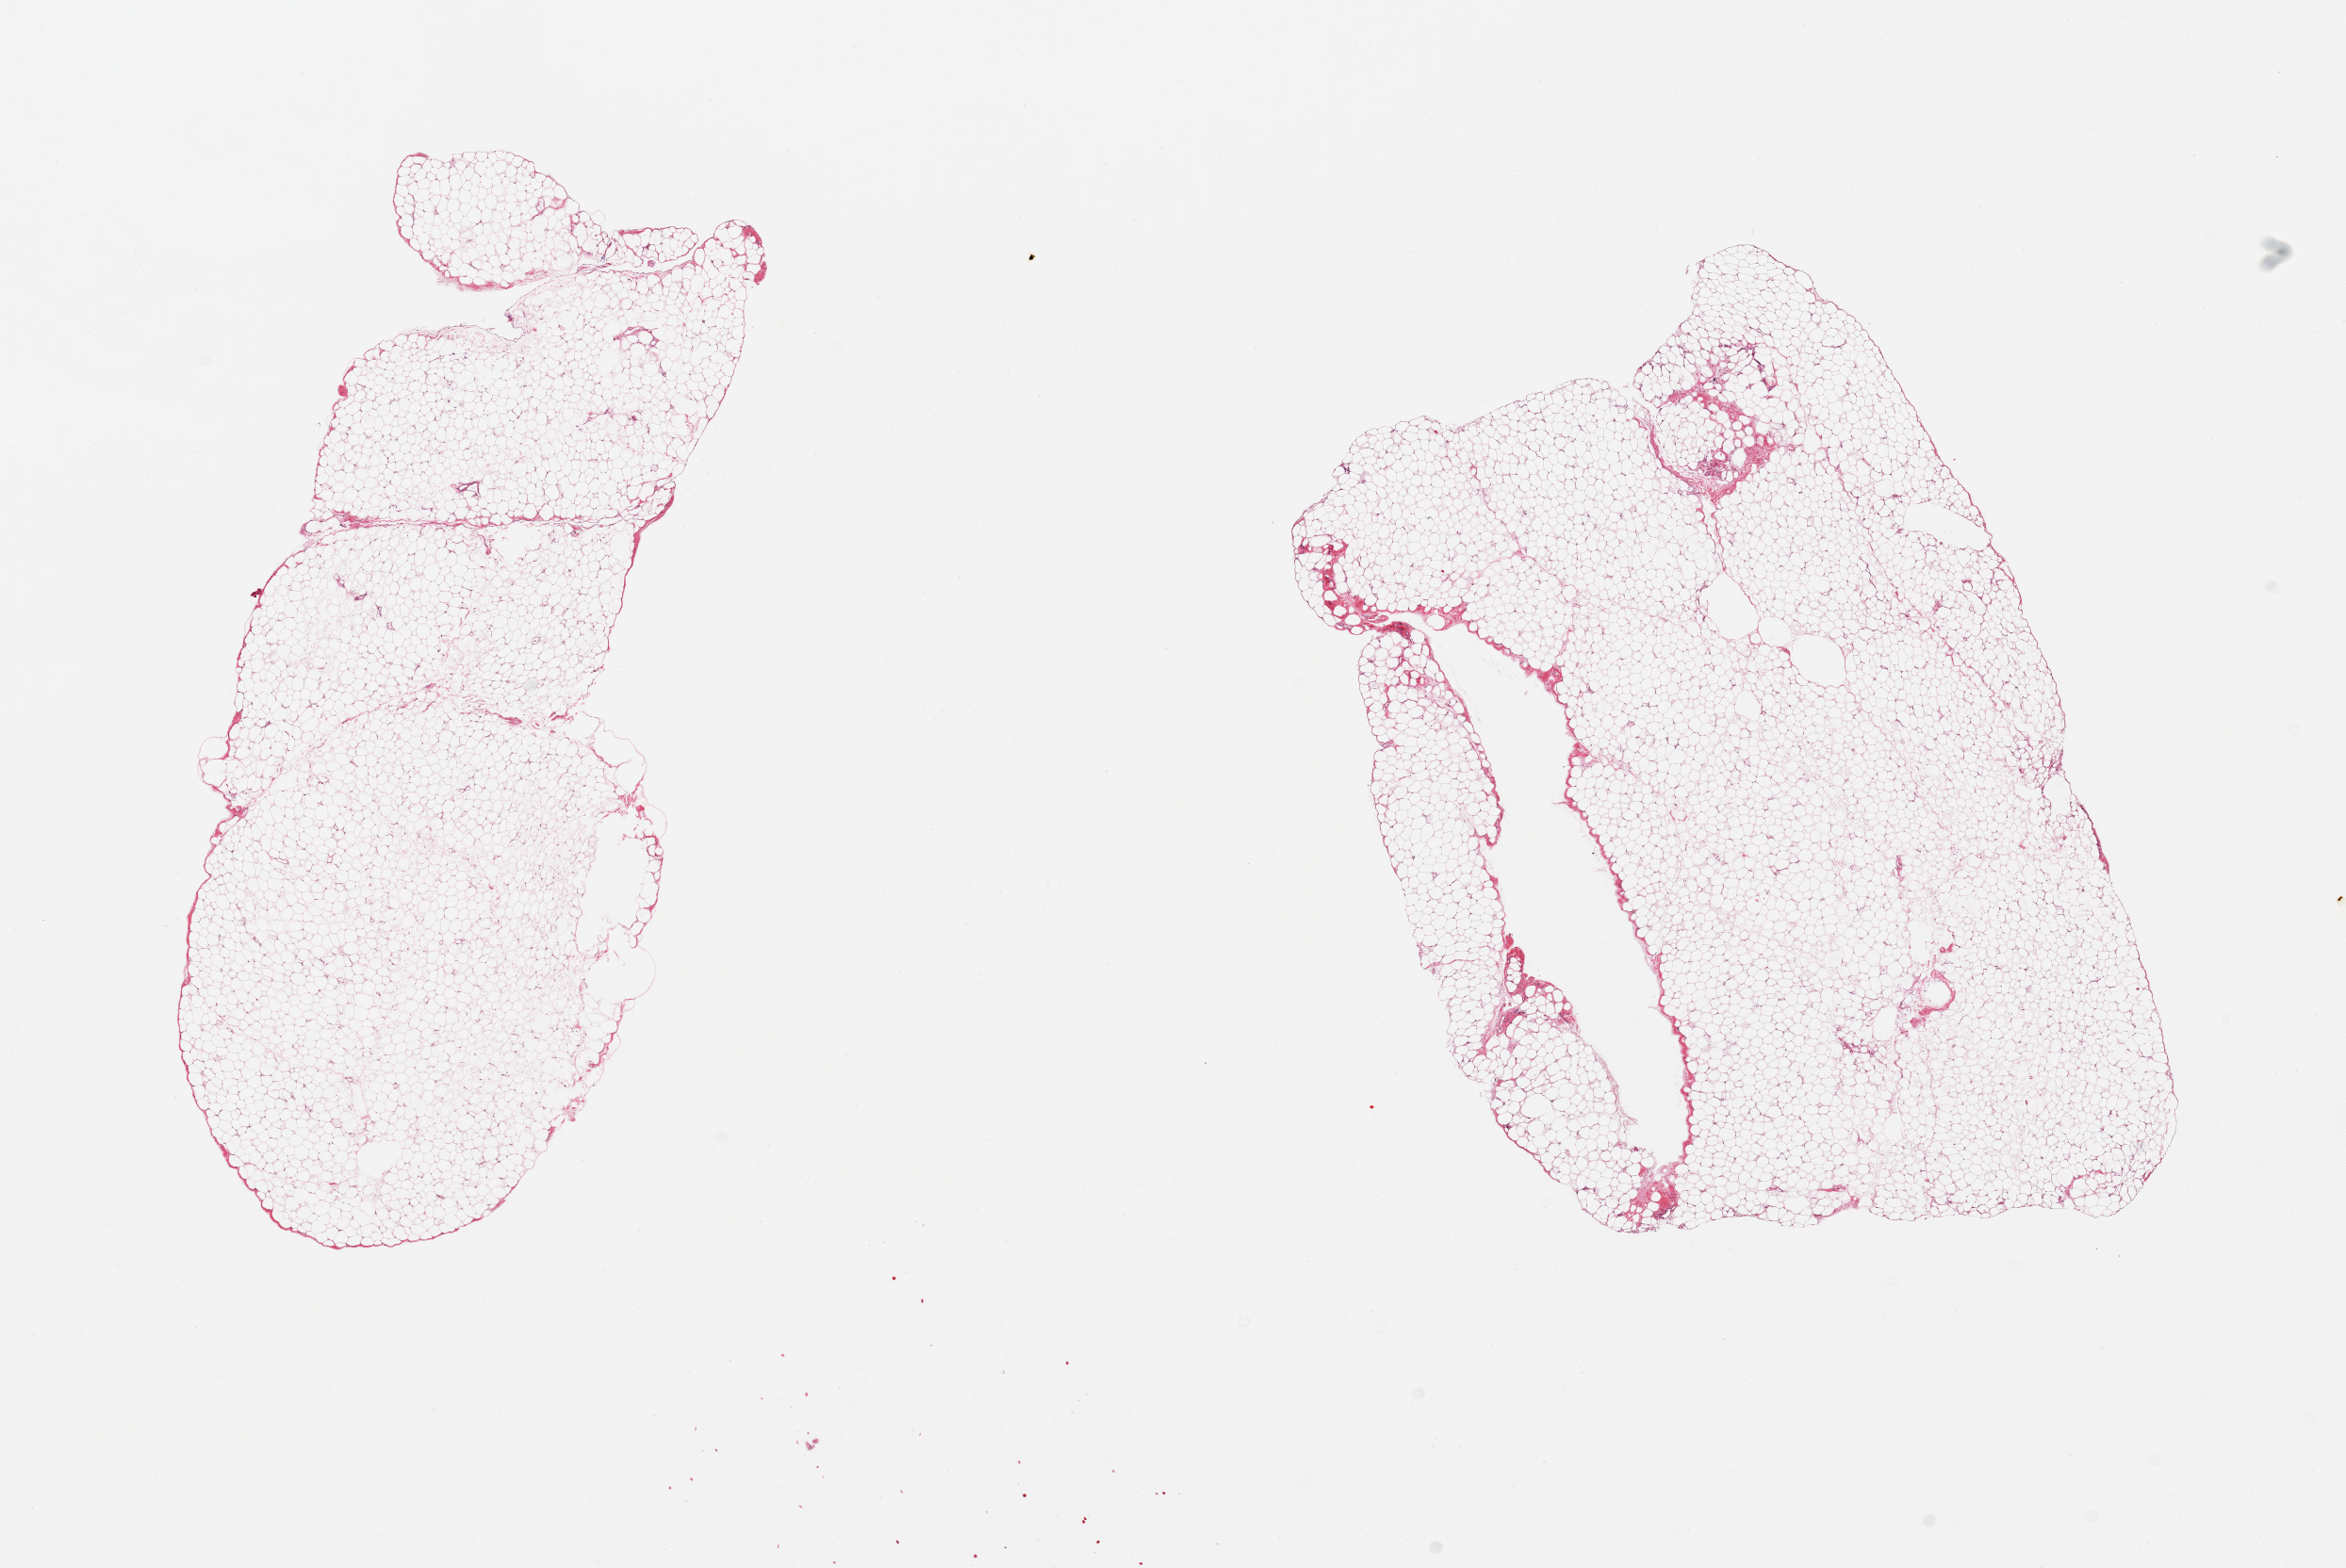
Haematoxylin and eosin whole-slide image, shown as a low-resolution overview of the whole scanned area (about 19.7 x 13.2 mm), PAXgene-fixed, paraffin-embedded tissue, section of omentum (target tissue), donor tissue sample. Donor: male.
Pathologist's review note for this sample: 2 pieces.